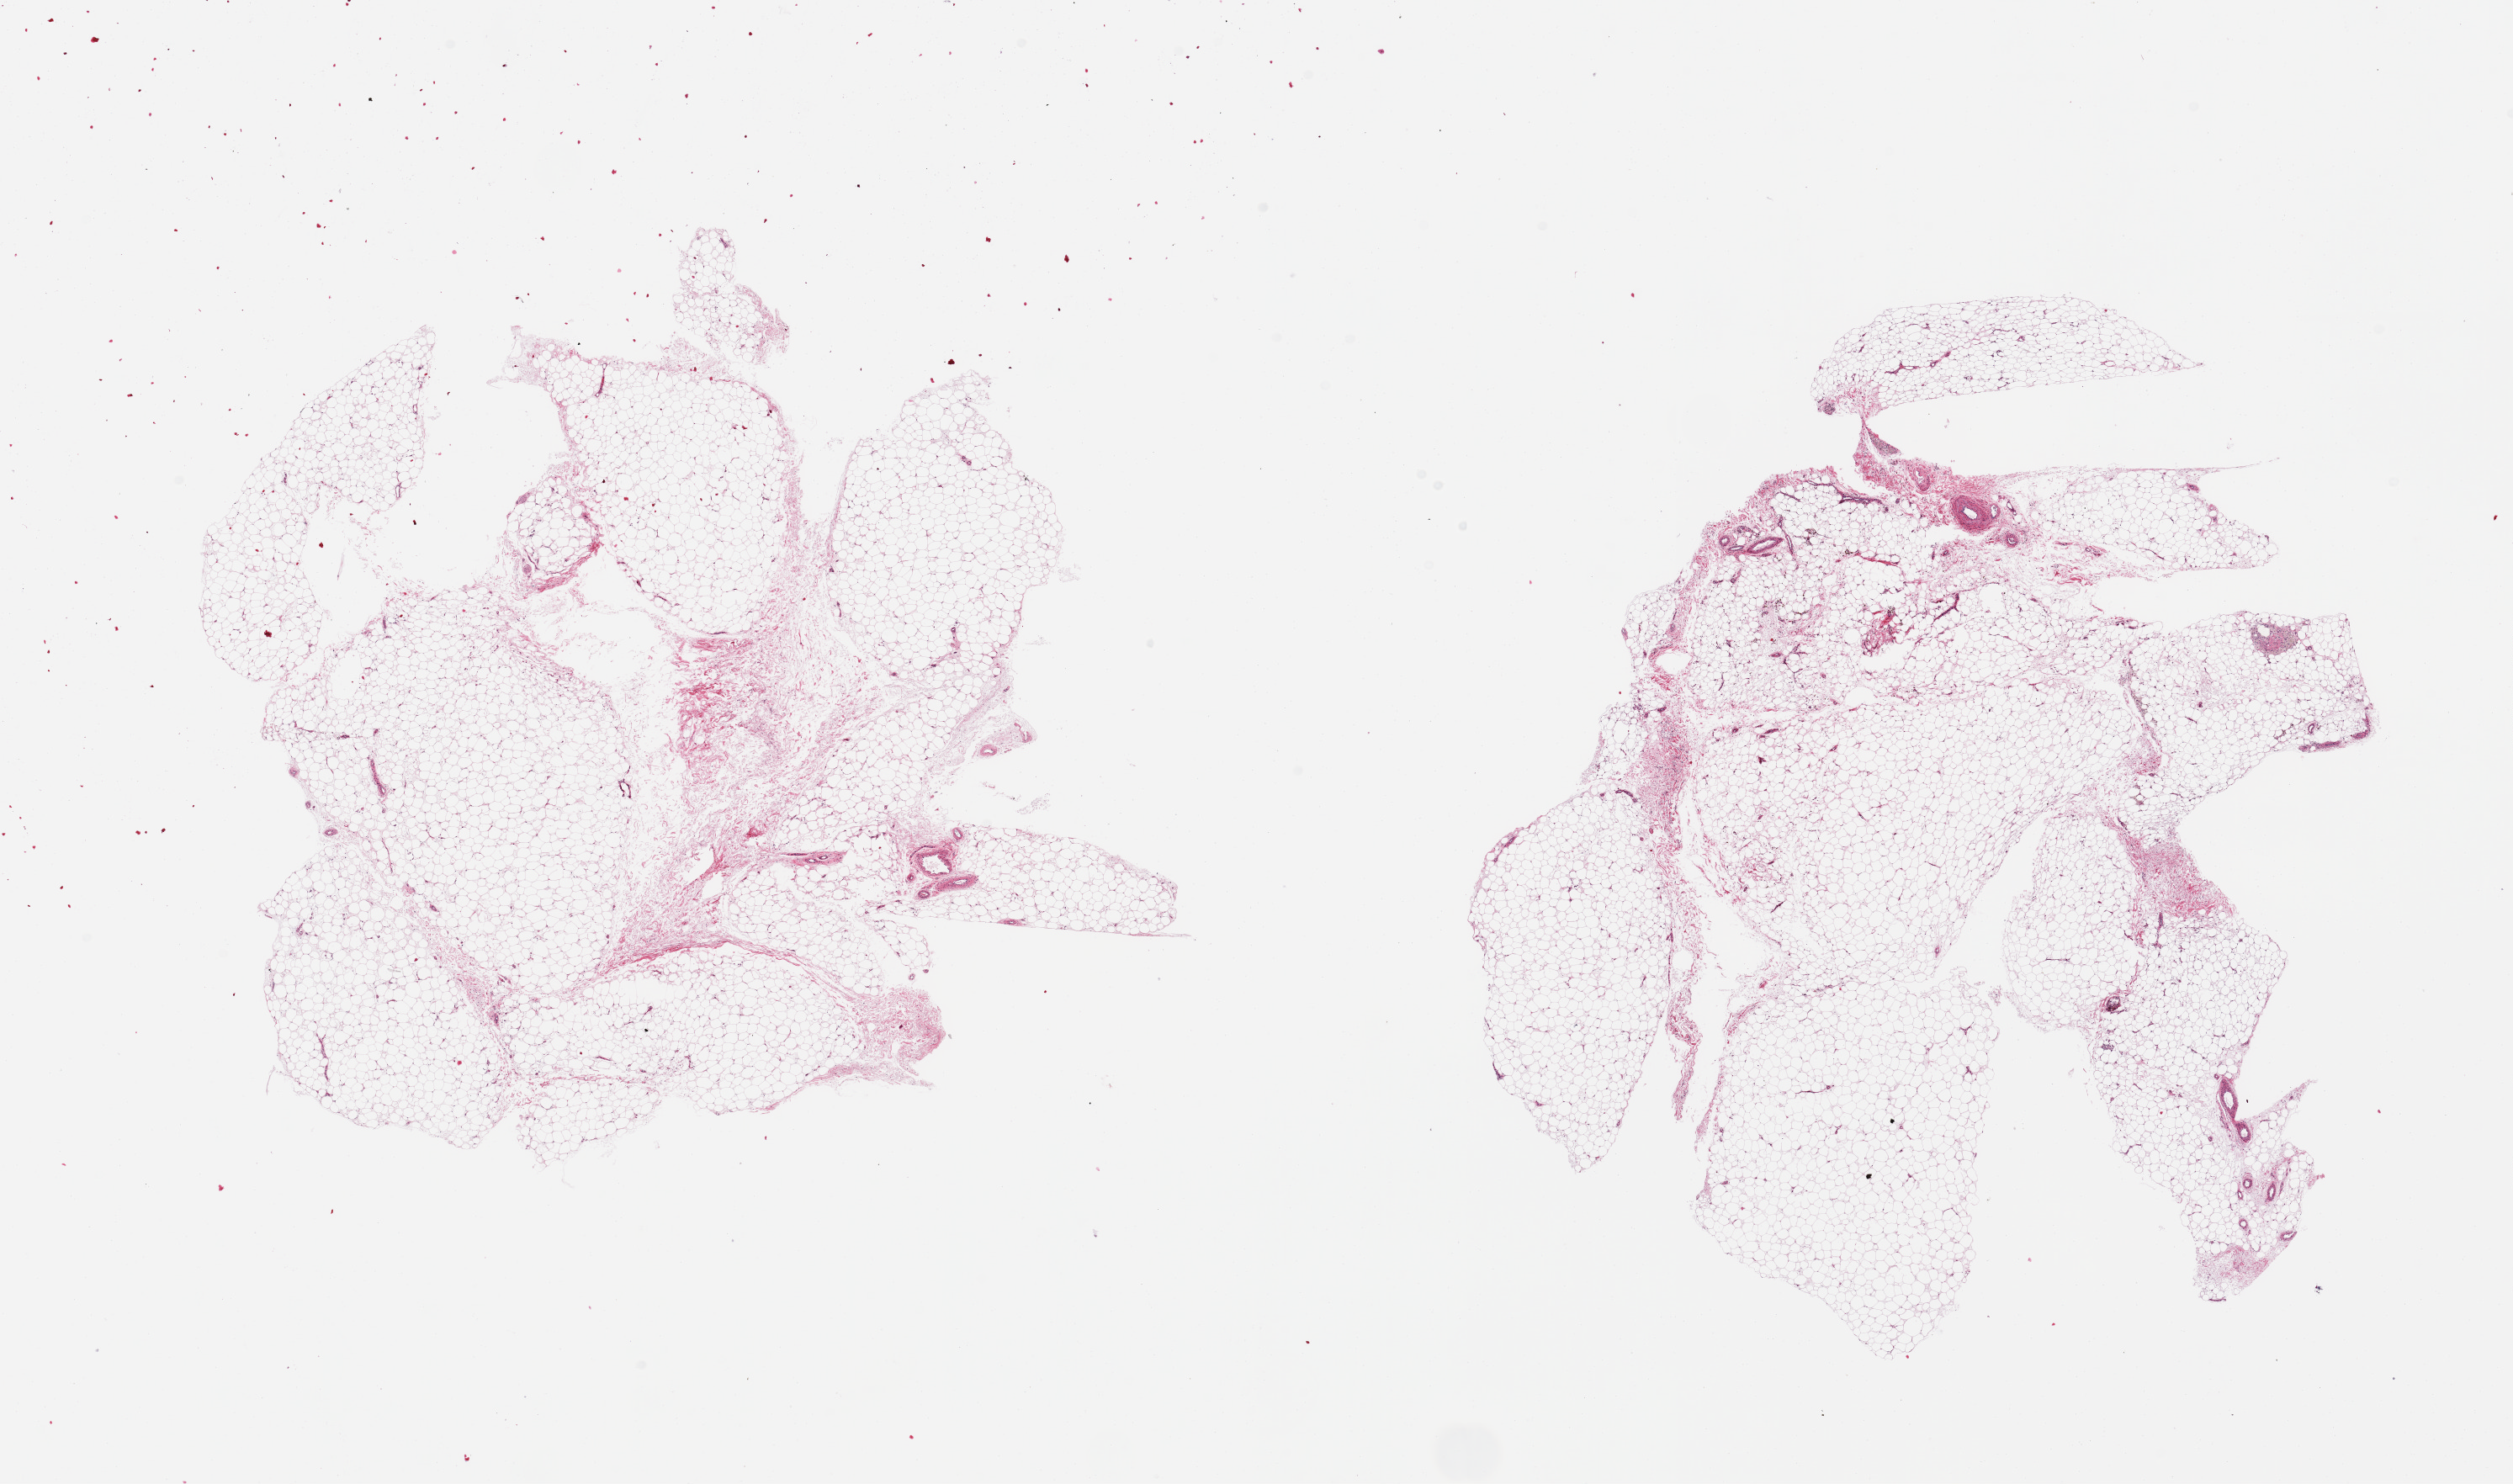
Whole-slide image, hematoxylin and eosin (H&E) stain — a low-resolution overview of the entire scanned area, about 23.6 x 14.0 mm, PAXgene-fixed paraffin-embedded (PFPE) section, section of adipose tissue (target tissue), tissue donor sample. Female donor.
- pathologist's review note for this sample: 2 pieces, fascia/vascular elements are ~10% of tissue; focal fat necrosis